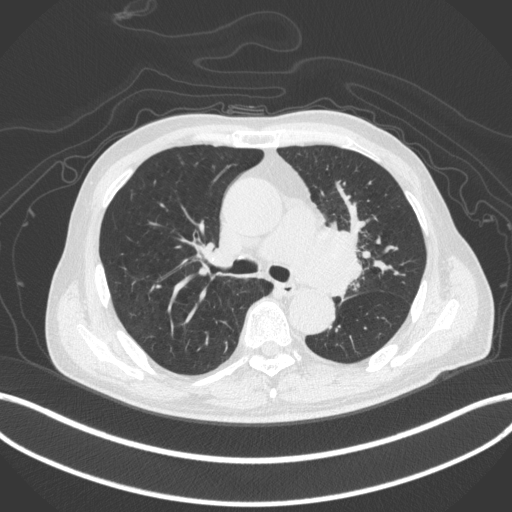
Chest CT, one axial slice; slice 275 of 420 in the series (ordered by position); reconstruction kernel B31f; 120 kVp; lung window (W 1500 / L -600 HU); 512 × 512 image matrix, field of view 400 × 400 mm. Male patient, age 77 years. From the clinical record (not read from this slice): clinical TNM (as recorded): T3 N1 M0.
Outlined on this slice (bounding box drawn by a radiologist):
- lung tumour (recorded histology: adenocarcinoma): bounding box <304,218,365,297> (left, top, right, bottom; pixels)